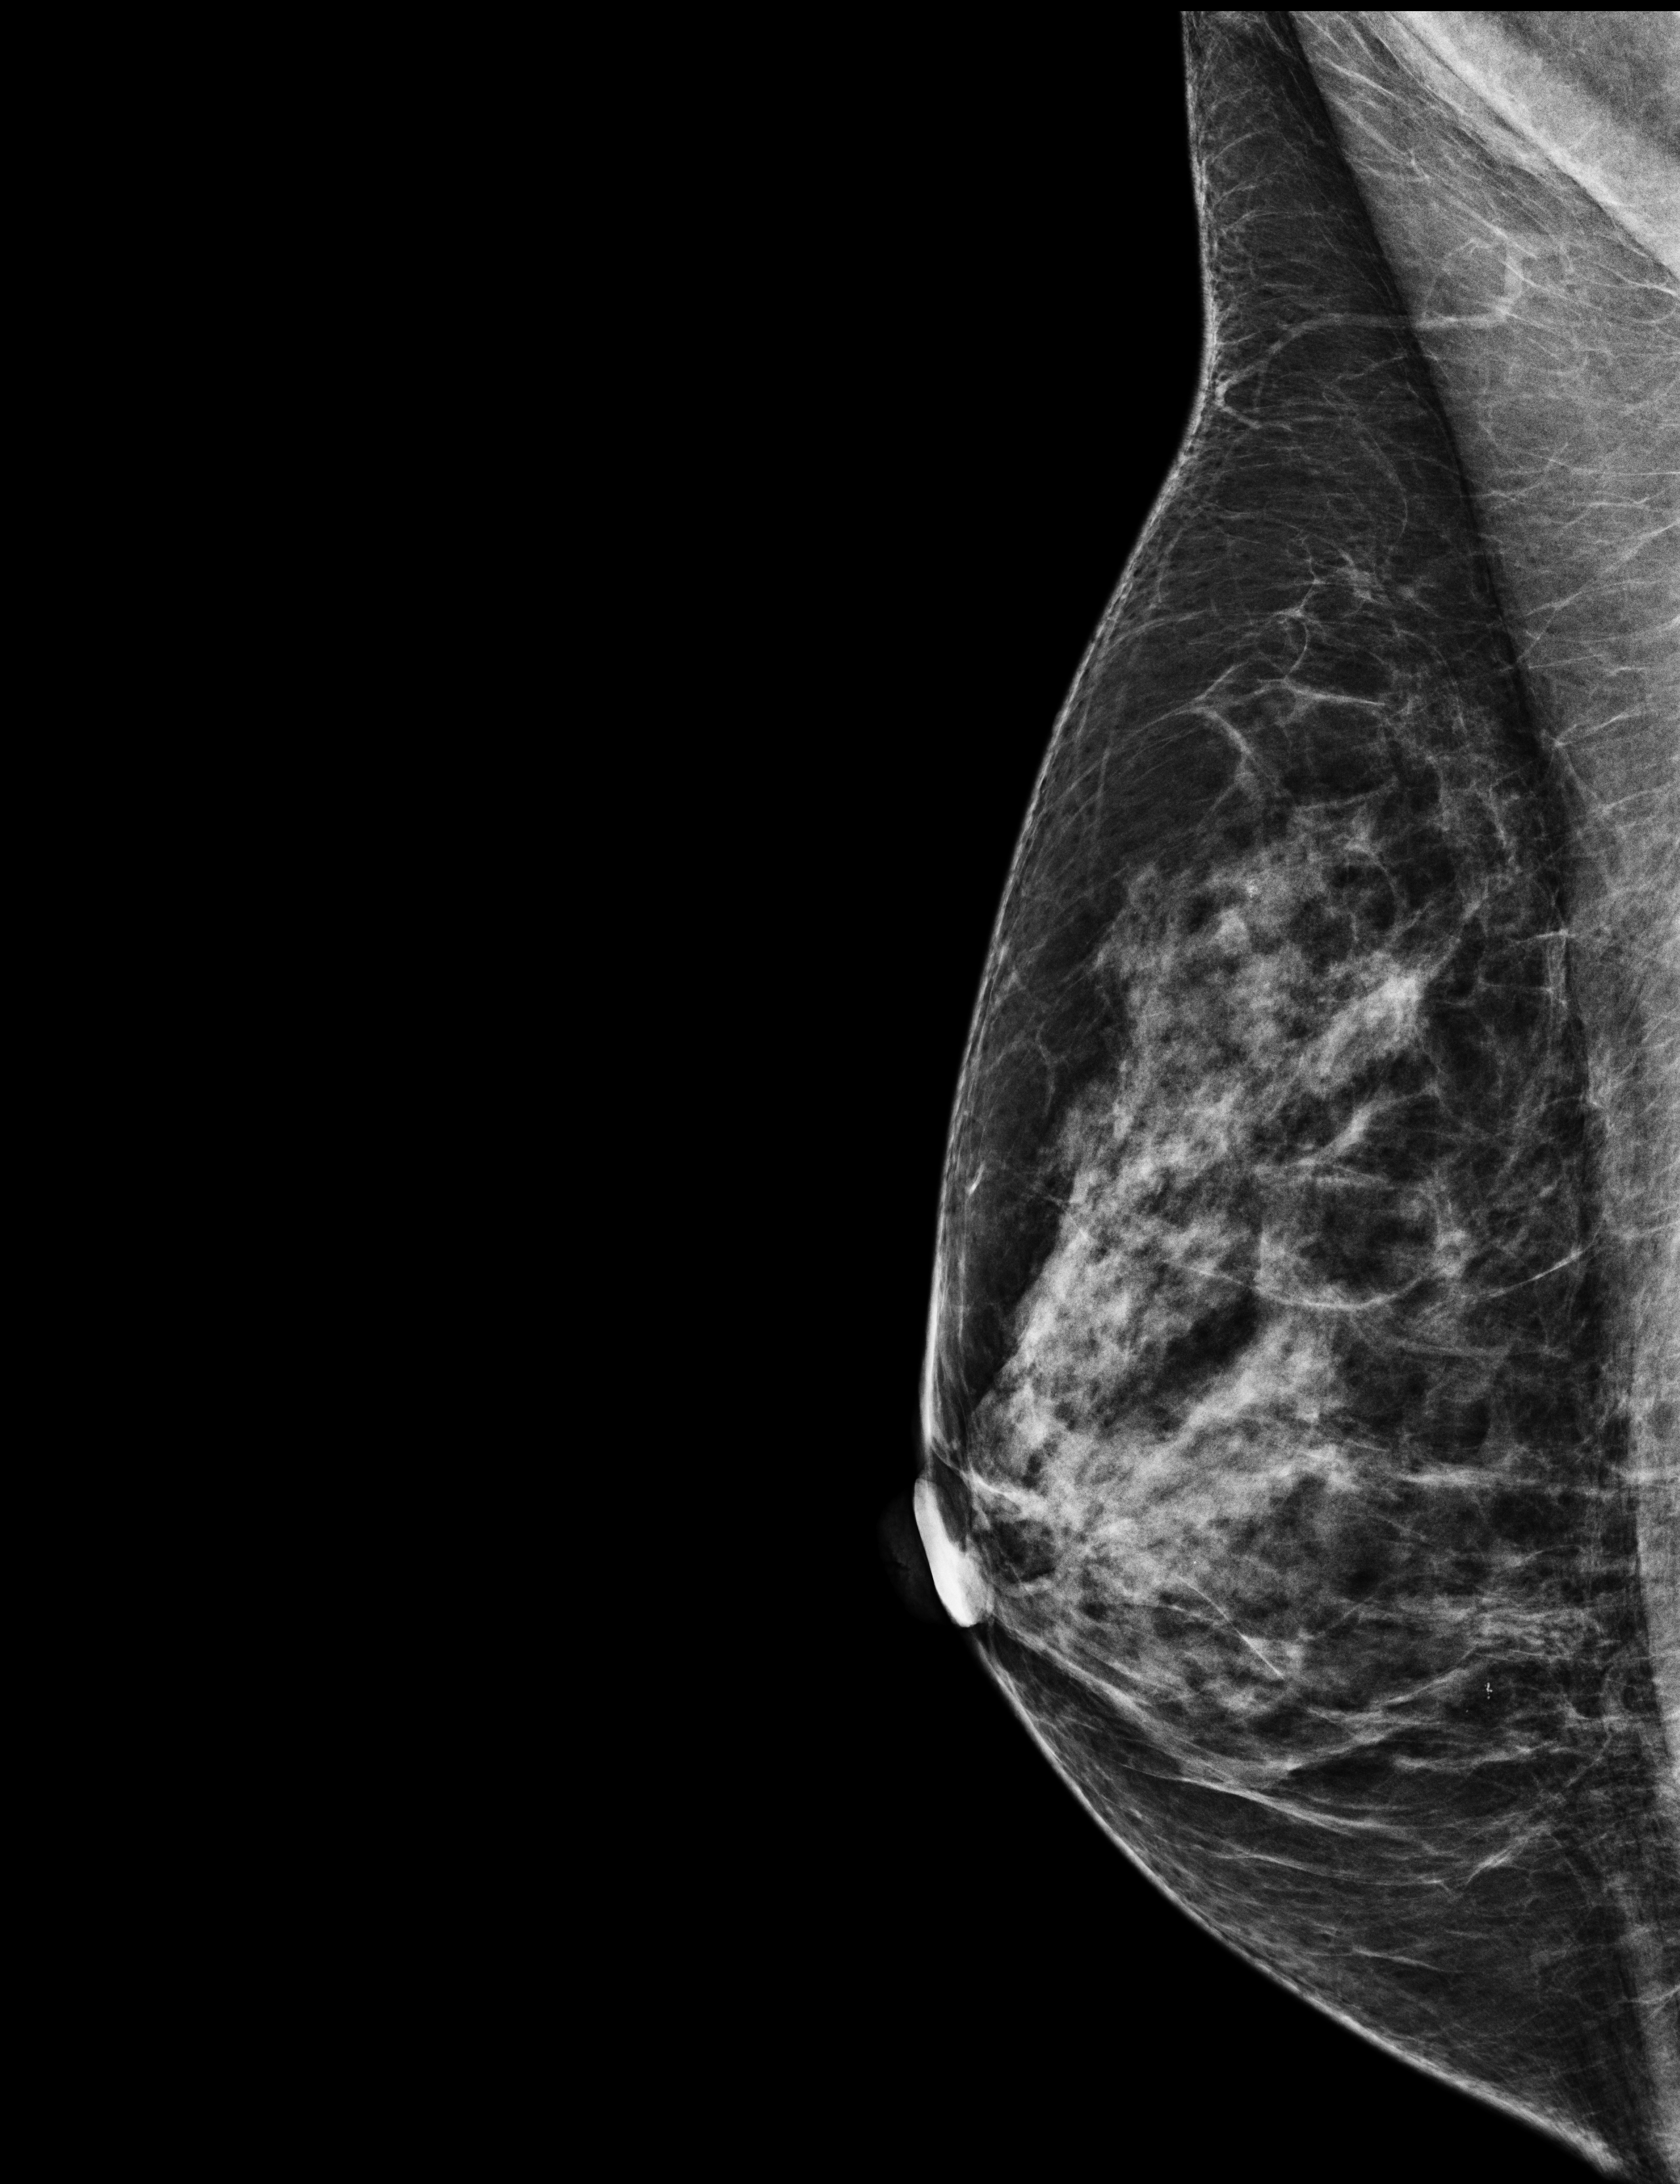
Full-field digital mammogram (FFDM), right breast, MLO view, screening examination, system: Selenia Dimensions. Patient: female, 60 years.
Breast density at the screening exam (both breasts): heterogeneously dense (BI-RADS density category c). Final BI-RADS category for the screening round (tomosynthesis exam, both breasts): category 1. Recall: recalled for additional imaging after this screen.